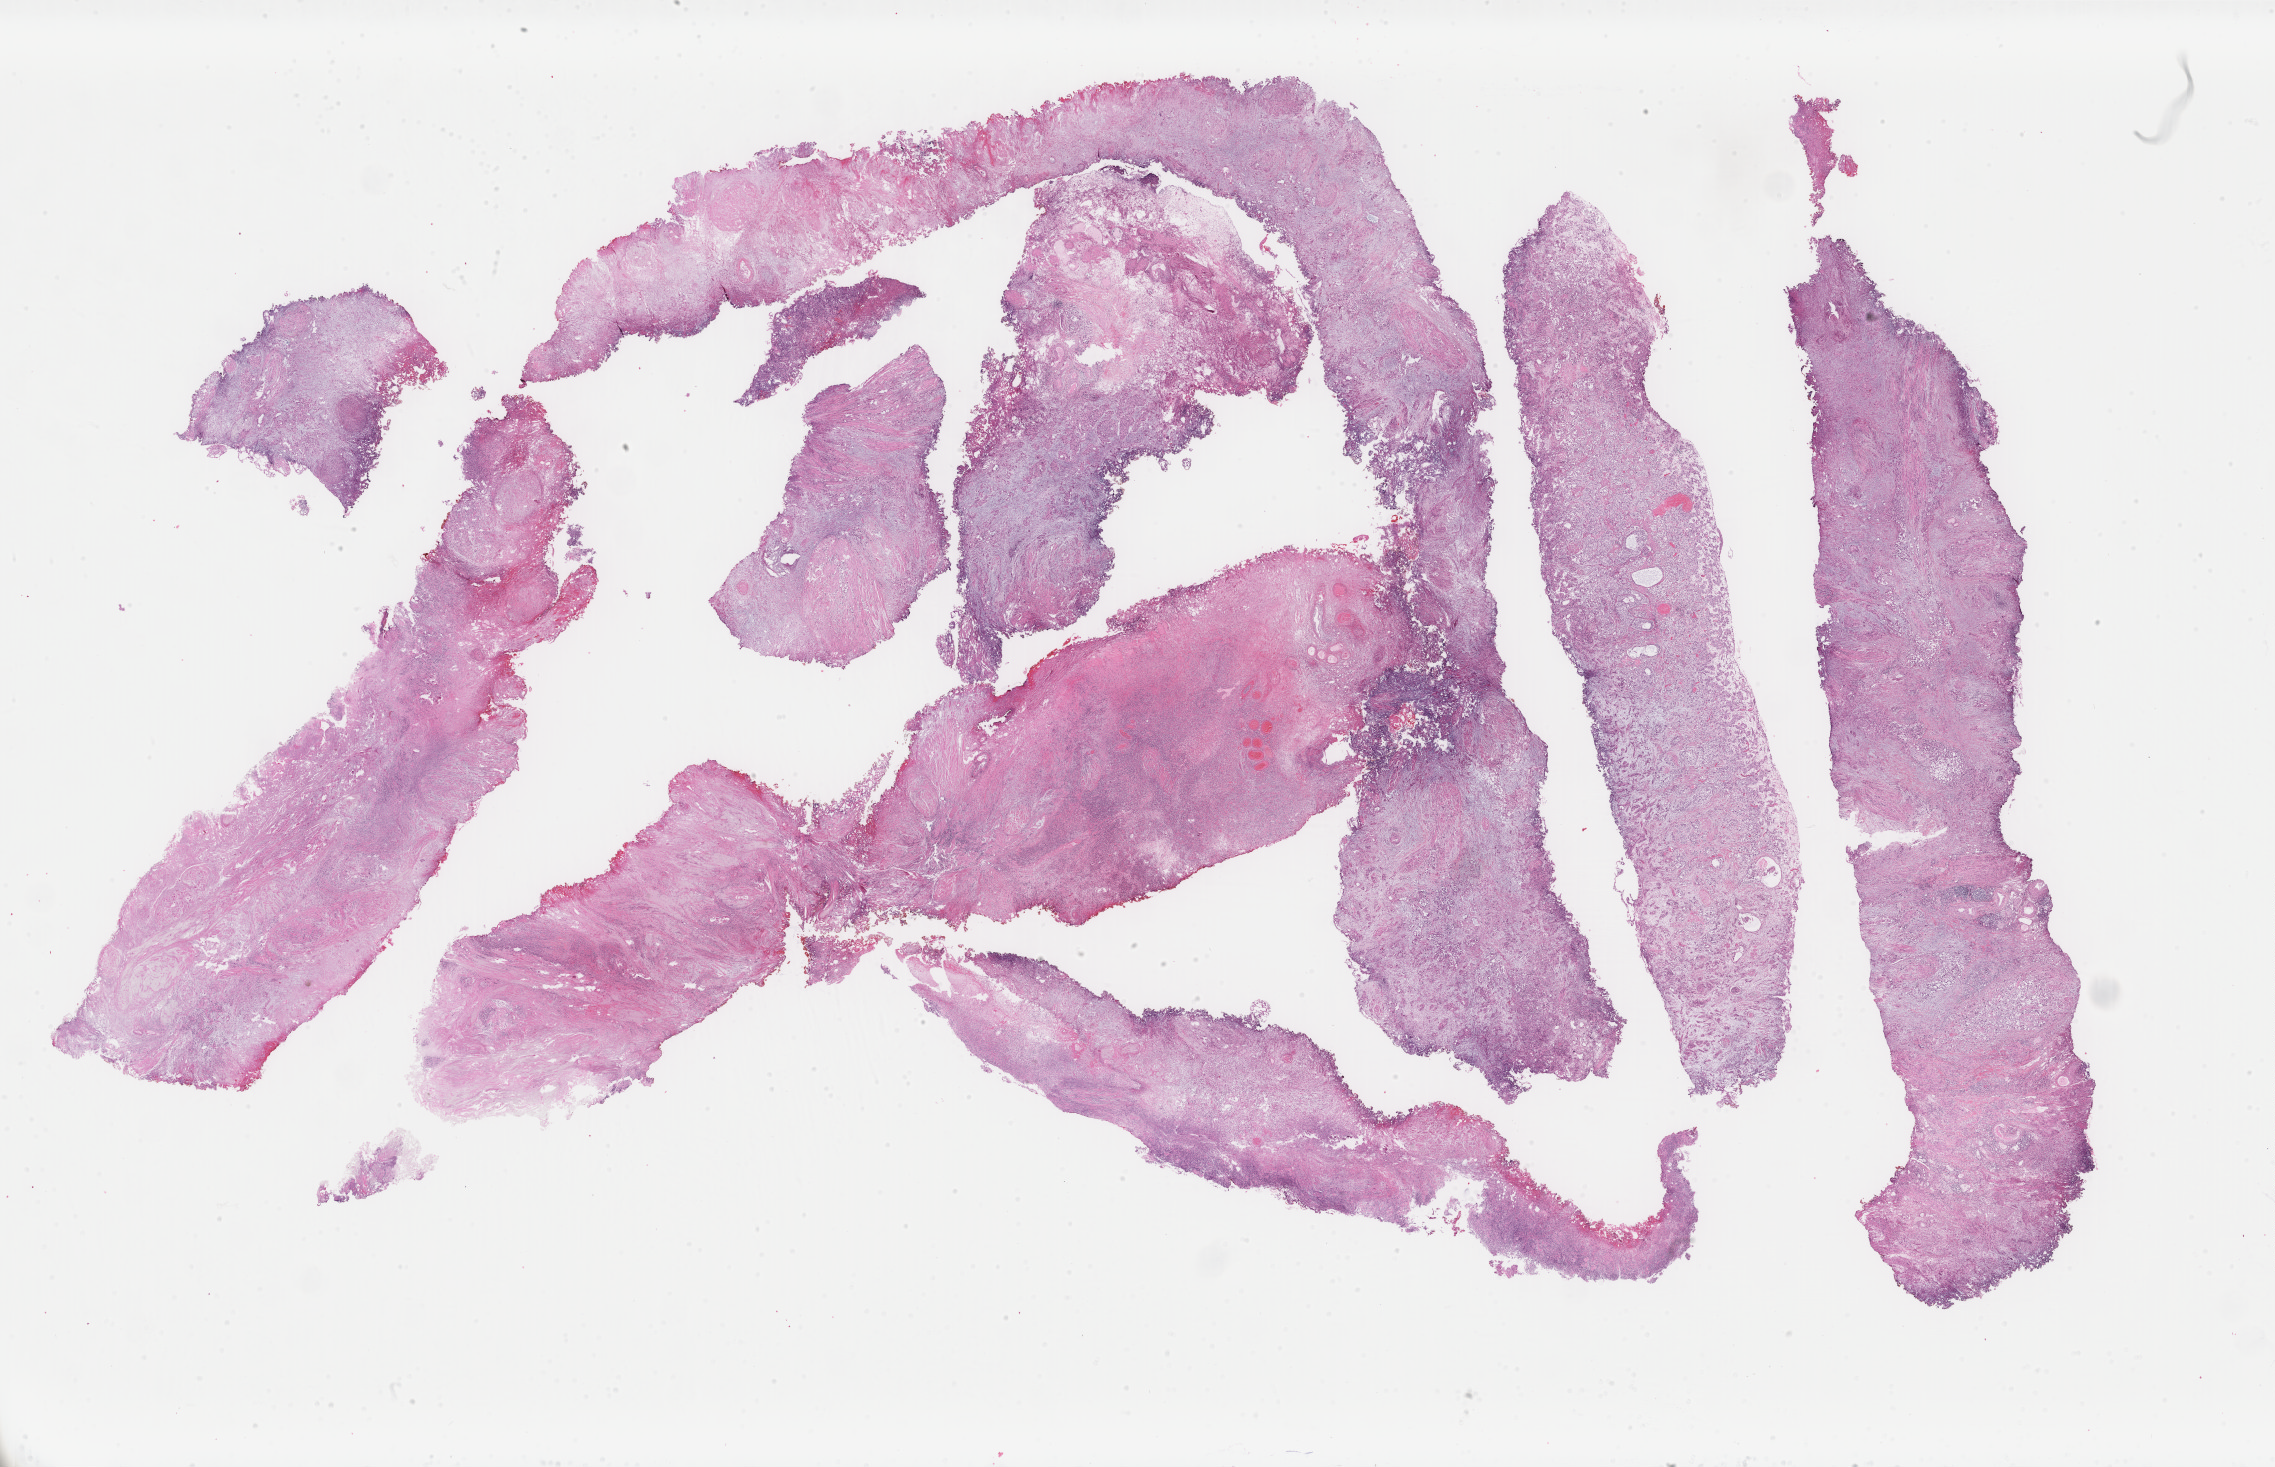
Whole-slide histology image, H&E-stained — shown as a low-resolution overview of the whole scanned area (about 36.1 x 23.3 mm, slide scanned at 40x); formalin-fixed paraffin-embedded (FFPE) diagnostic section; bladder, primary tumour sample. Female patient; age at initial diagnosis 58 years. Histologic grade: high grade.
AJCC pathologic stage: II (2nd edition). Pathologic diagnosis: Transitional cell carcinoma.